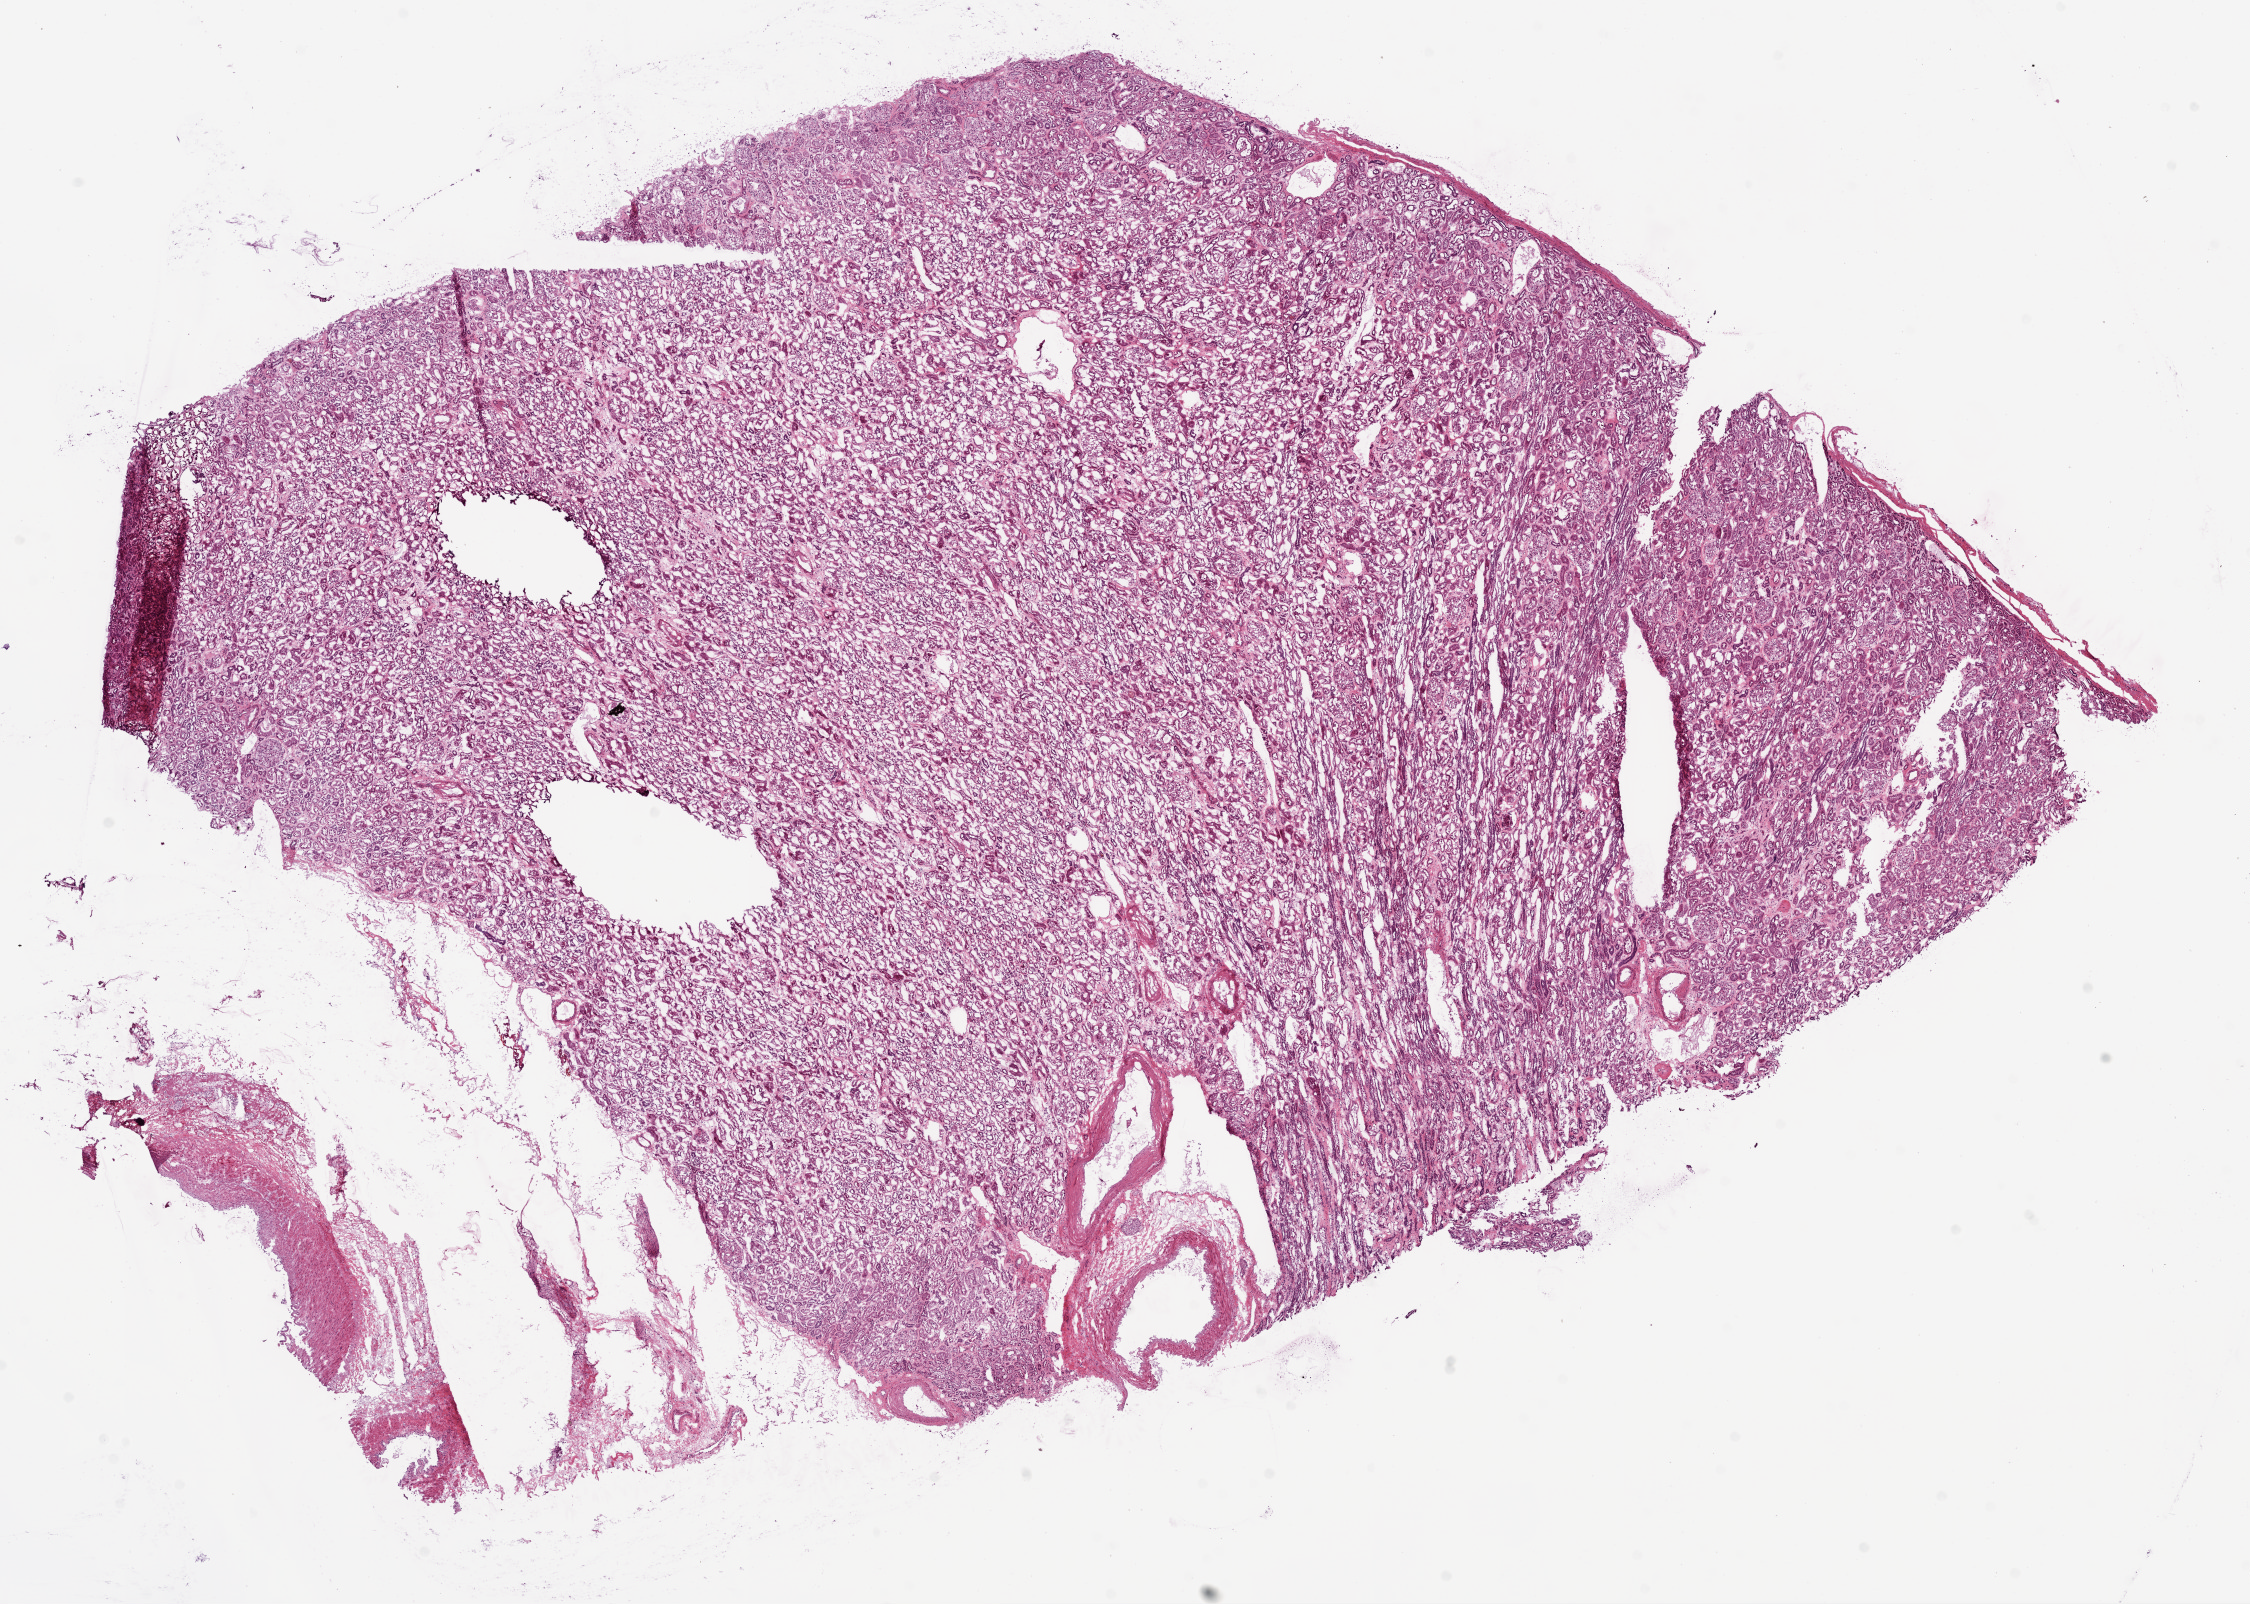
Hematoxylin and eosin (H&E) stained whole-slide image — shown as a low-resolution overview of the whole scanned area (about 18.1 x 12.9 mm). Frozen section. Kidney, solid tissue normal (non-tumour tissue) sample. Male, age 60 years at initial diagnosis.
* this section: solid tissue normal sample (biorepository sample class)
* patient diagnosis: Clear cell adenocarcinoma, NOS